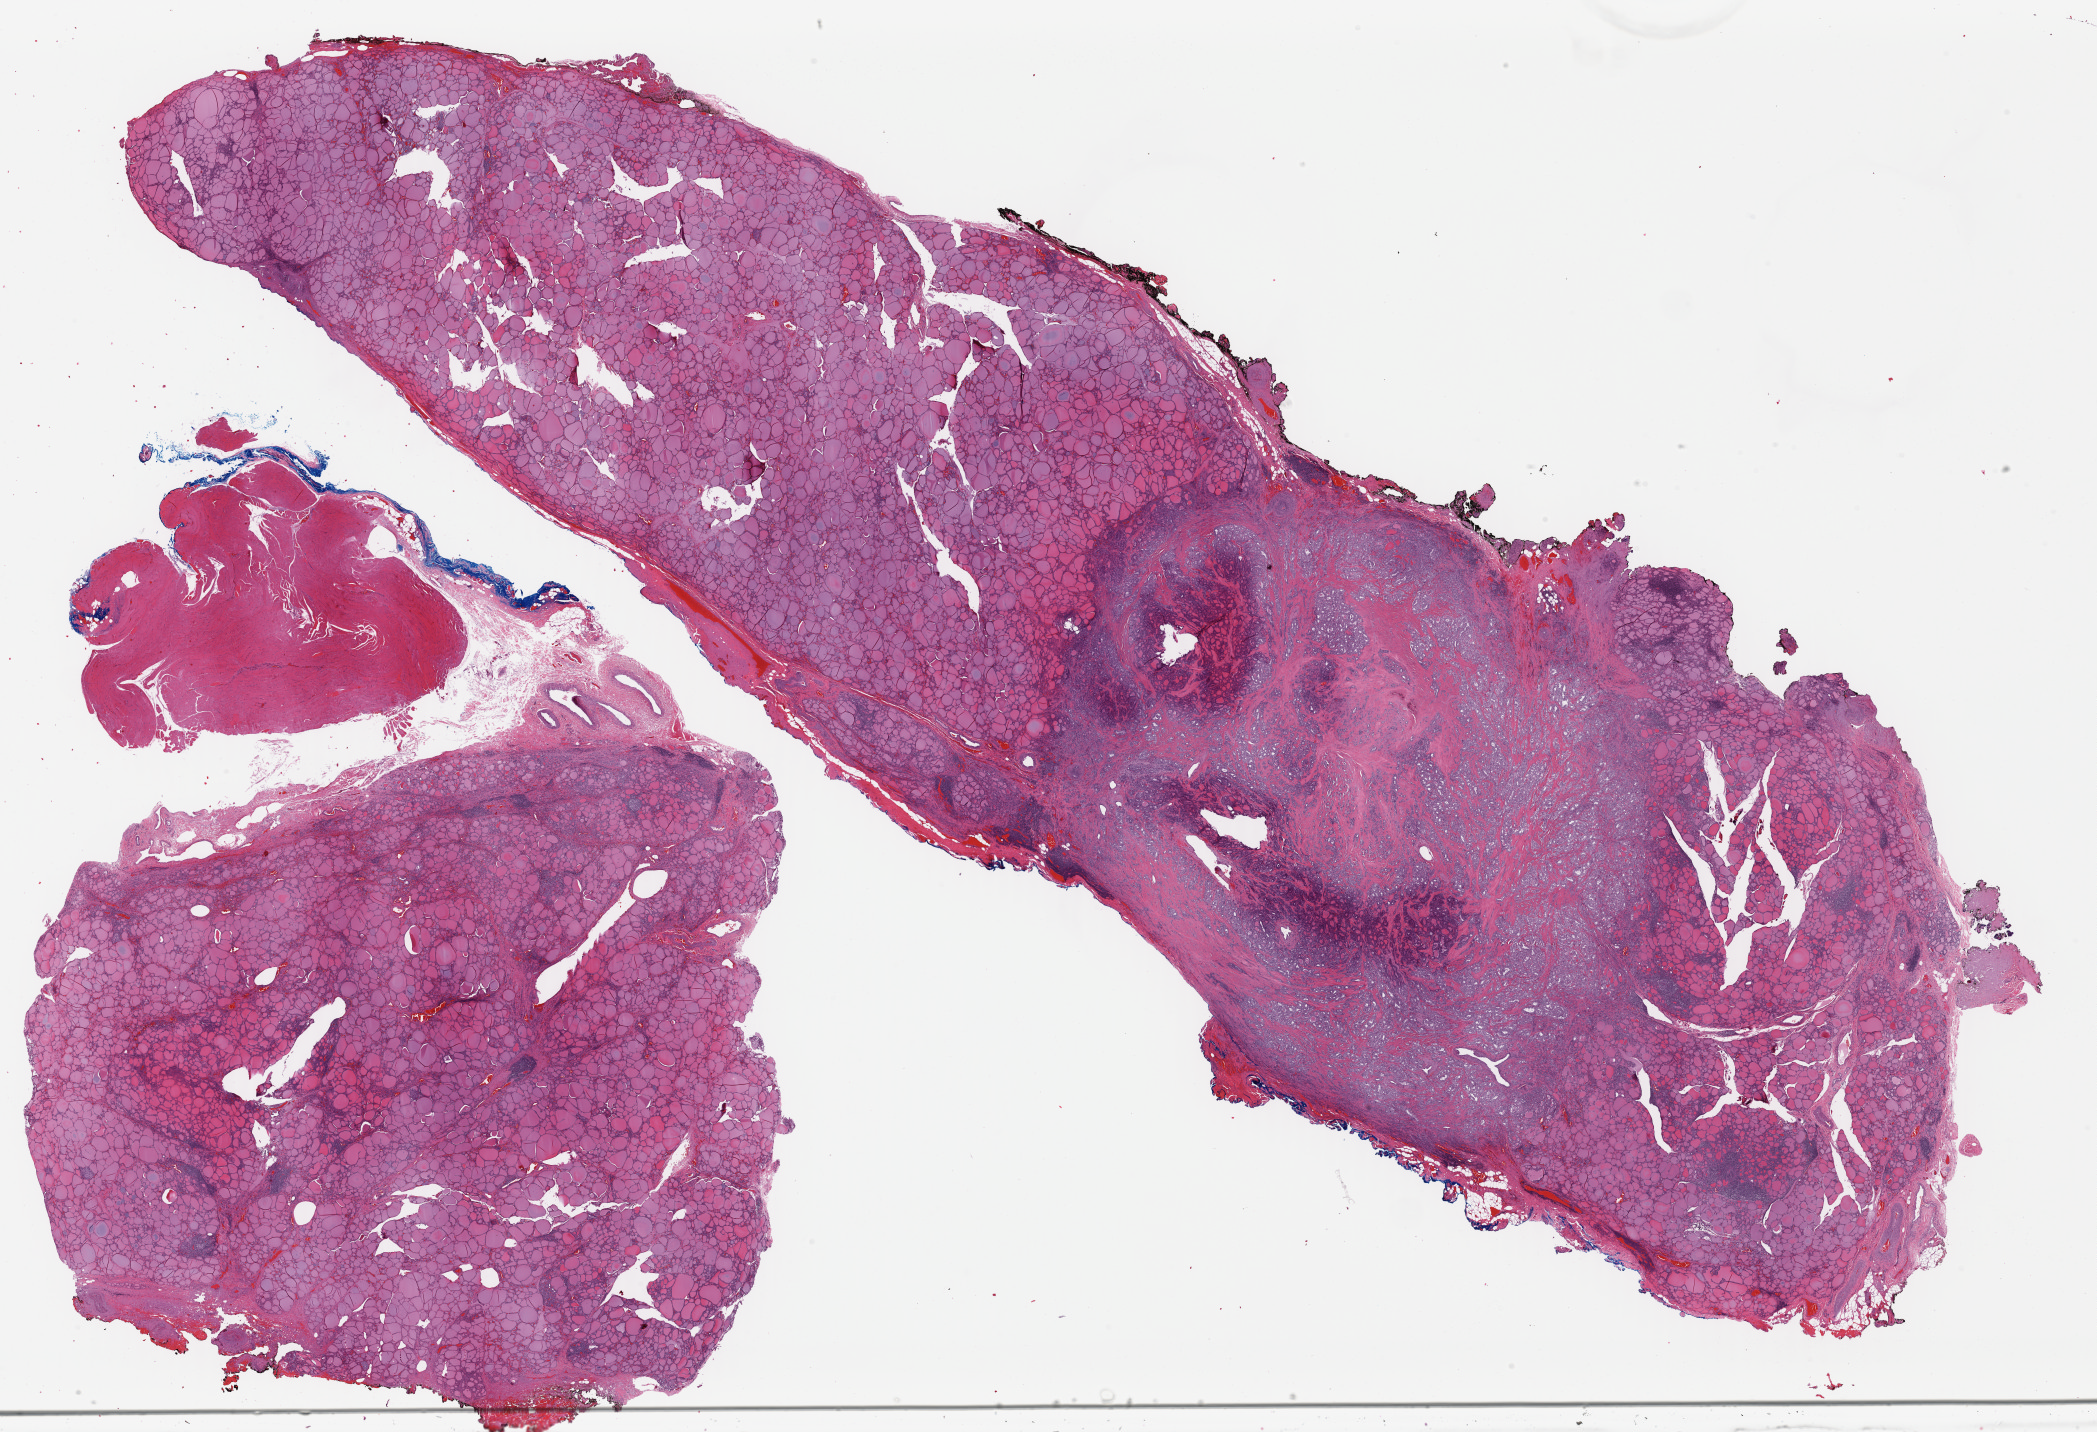
H&E-stained whole-slide image — low-resolution overview of the scanned area, about 33.1 x 22.6 mm (slide scanned at 40x); formalin-fixed paraffin-embedded (FFPE) diagnostic section; primary tumour sample from the thyroid. Female, age 49 years at initial diagnosis.
TNM: T3 N0 M0. AJCC pathologic stage: III (7th edition). Histologic diagnosis: Papillary adenocarcinoma, NOS (thyroid gland).